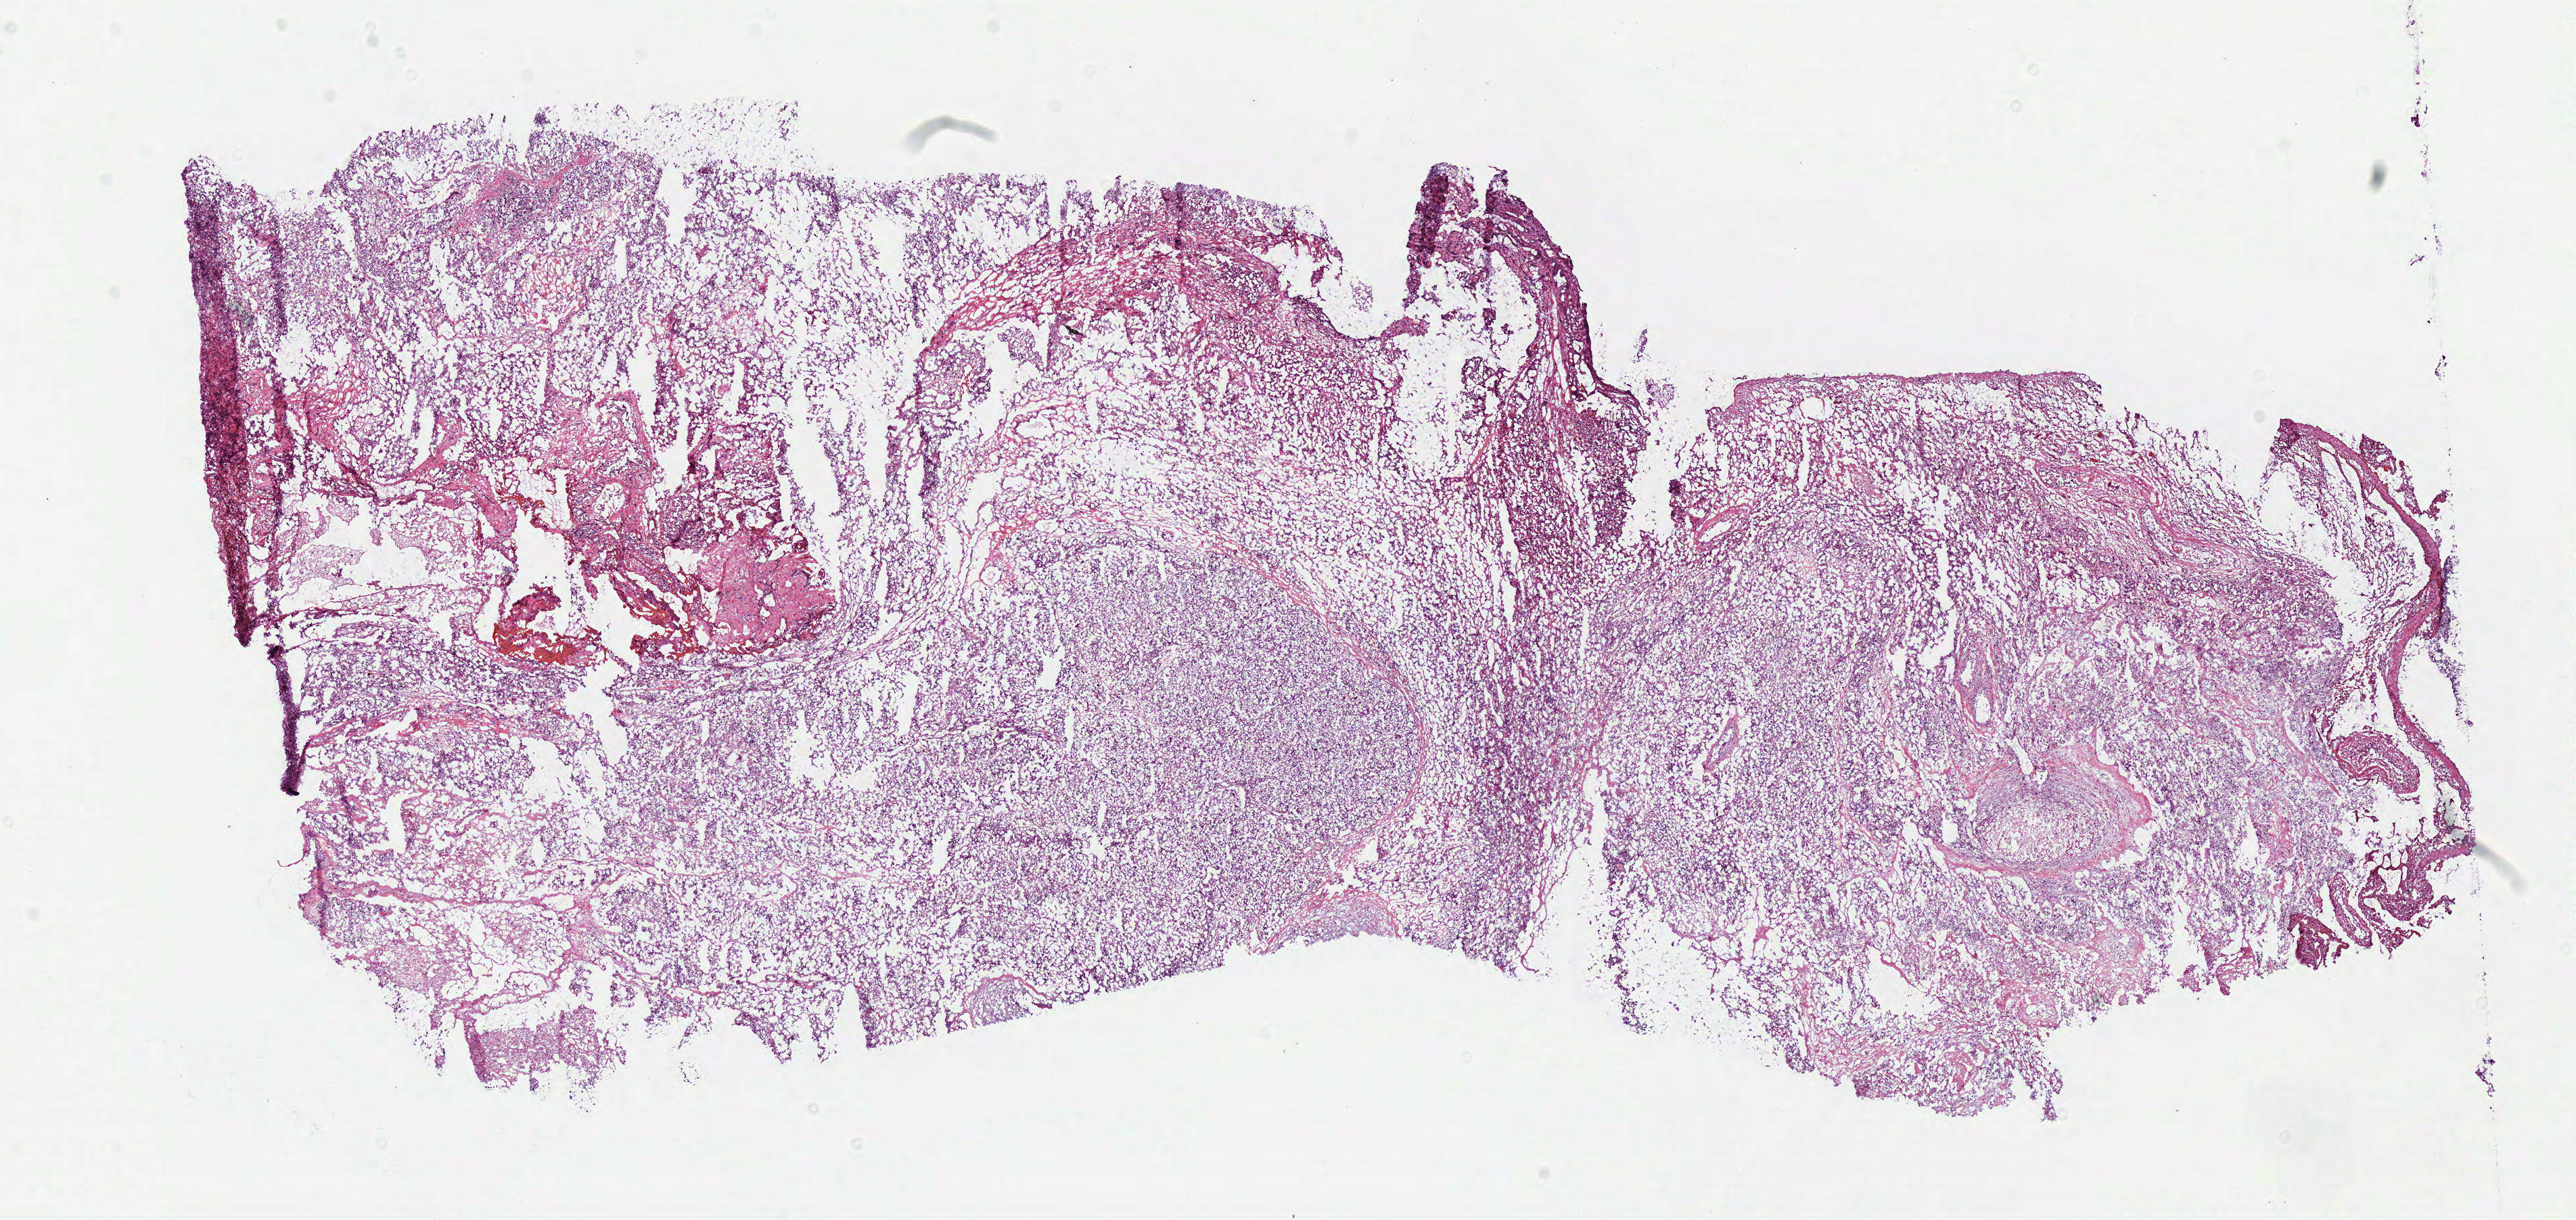
Digitized H&E tissue section (whole slide), shown as a low-resolution overview of the whole scanned area (about 15.0 x 7.1 mm, from a 40x scan); frozen section from the bottom of the tissue portion; primary tumour sample from the brain. Male patient; age at initial diagnosis 57 years. Composition of this section per pathologist review: tumour cells 85%, tumour nuclei 80%, normal cells 0%, stromal cells 15%, necrosis 0%.
- diagnosis: Glioblastoma